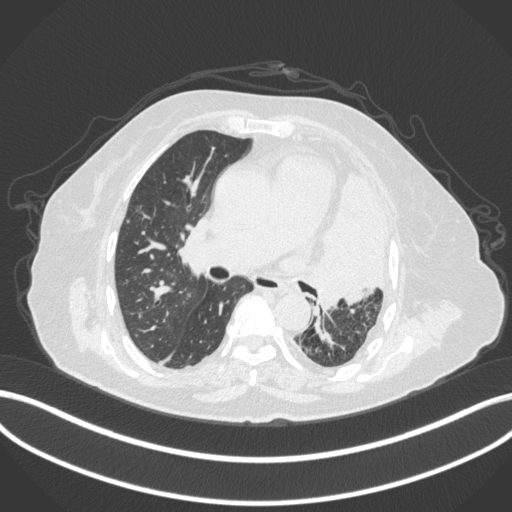
Chest CT, one axial slice; position 216 of 399 along the scan axis; 120 kVp; lung window (W 1500 / L -600 HU); 1 mm slice thickness; 512 × 512 image matrix, field of view 400 × 400 mm. Patient: female, 75 years. Case-level facts recorded for this patient, not image findings: clinical TNM (as recorded): T3 N3 M1.
Outlined on this slice (rectangle marked by the reading radiologist):
- lung tumour (recorded histology: adenocarcinoma): bounding box (x1, y1, x2, y2) in pixels: (305, 175, 388, 313)